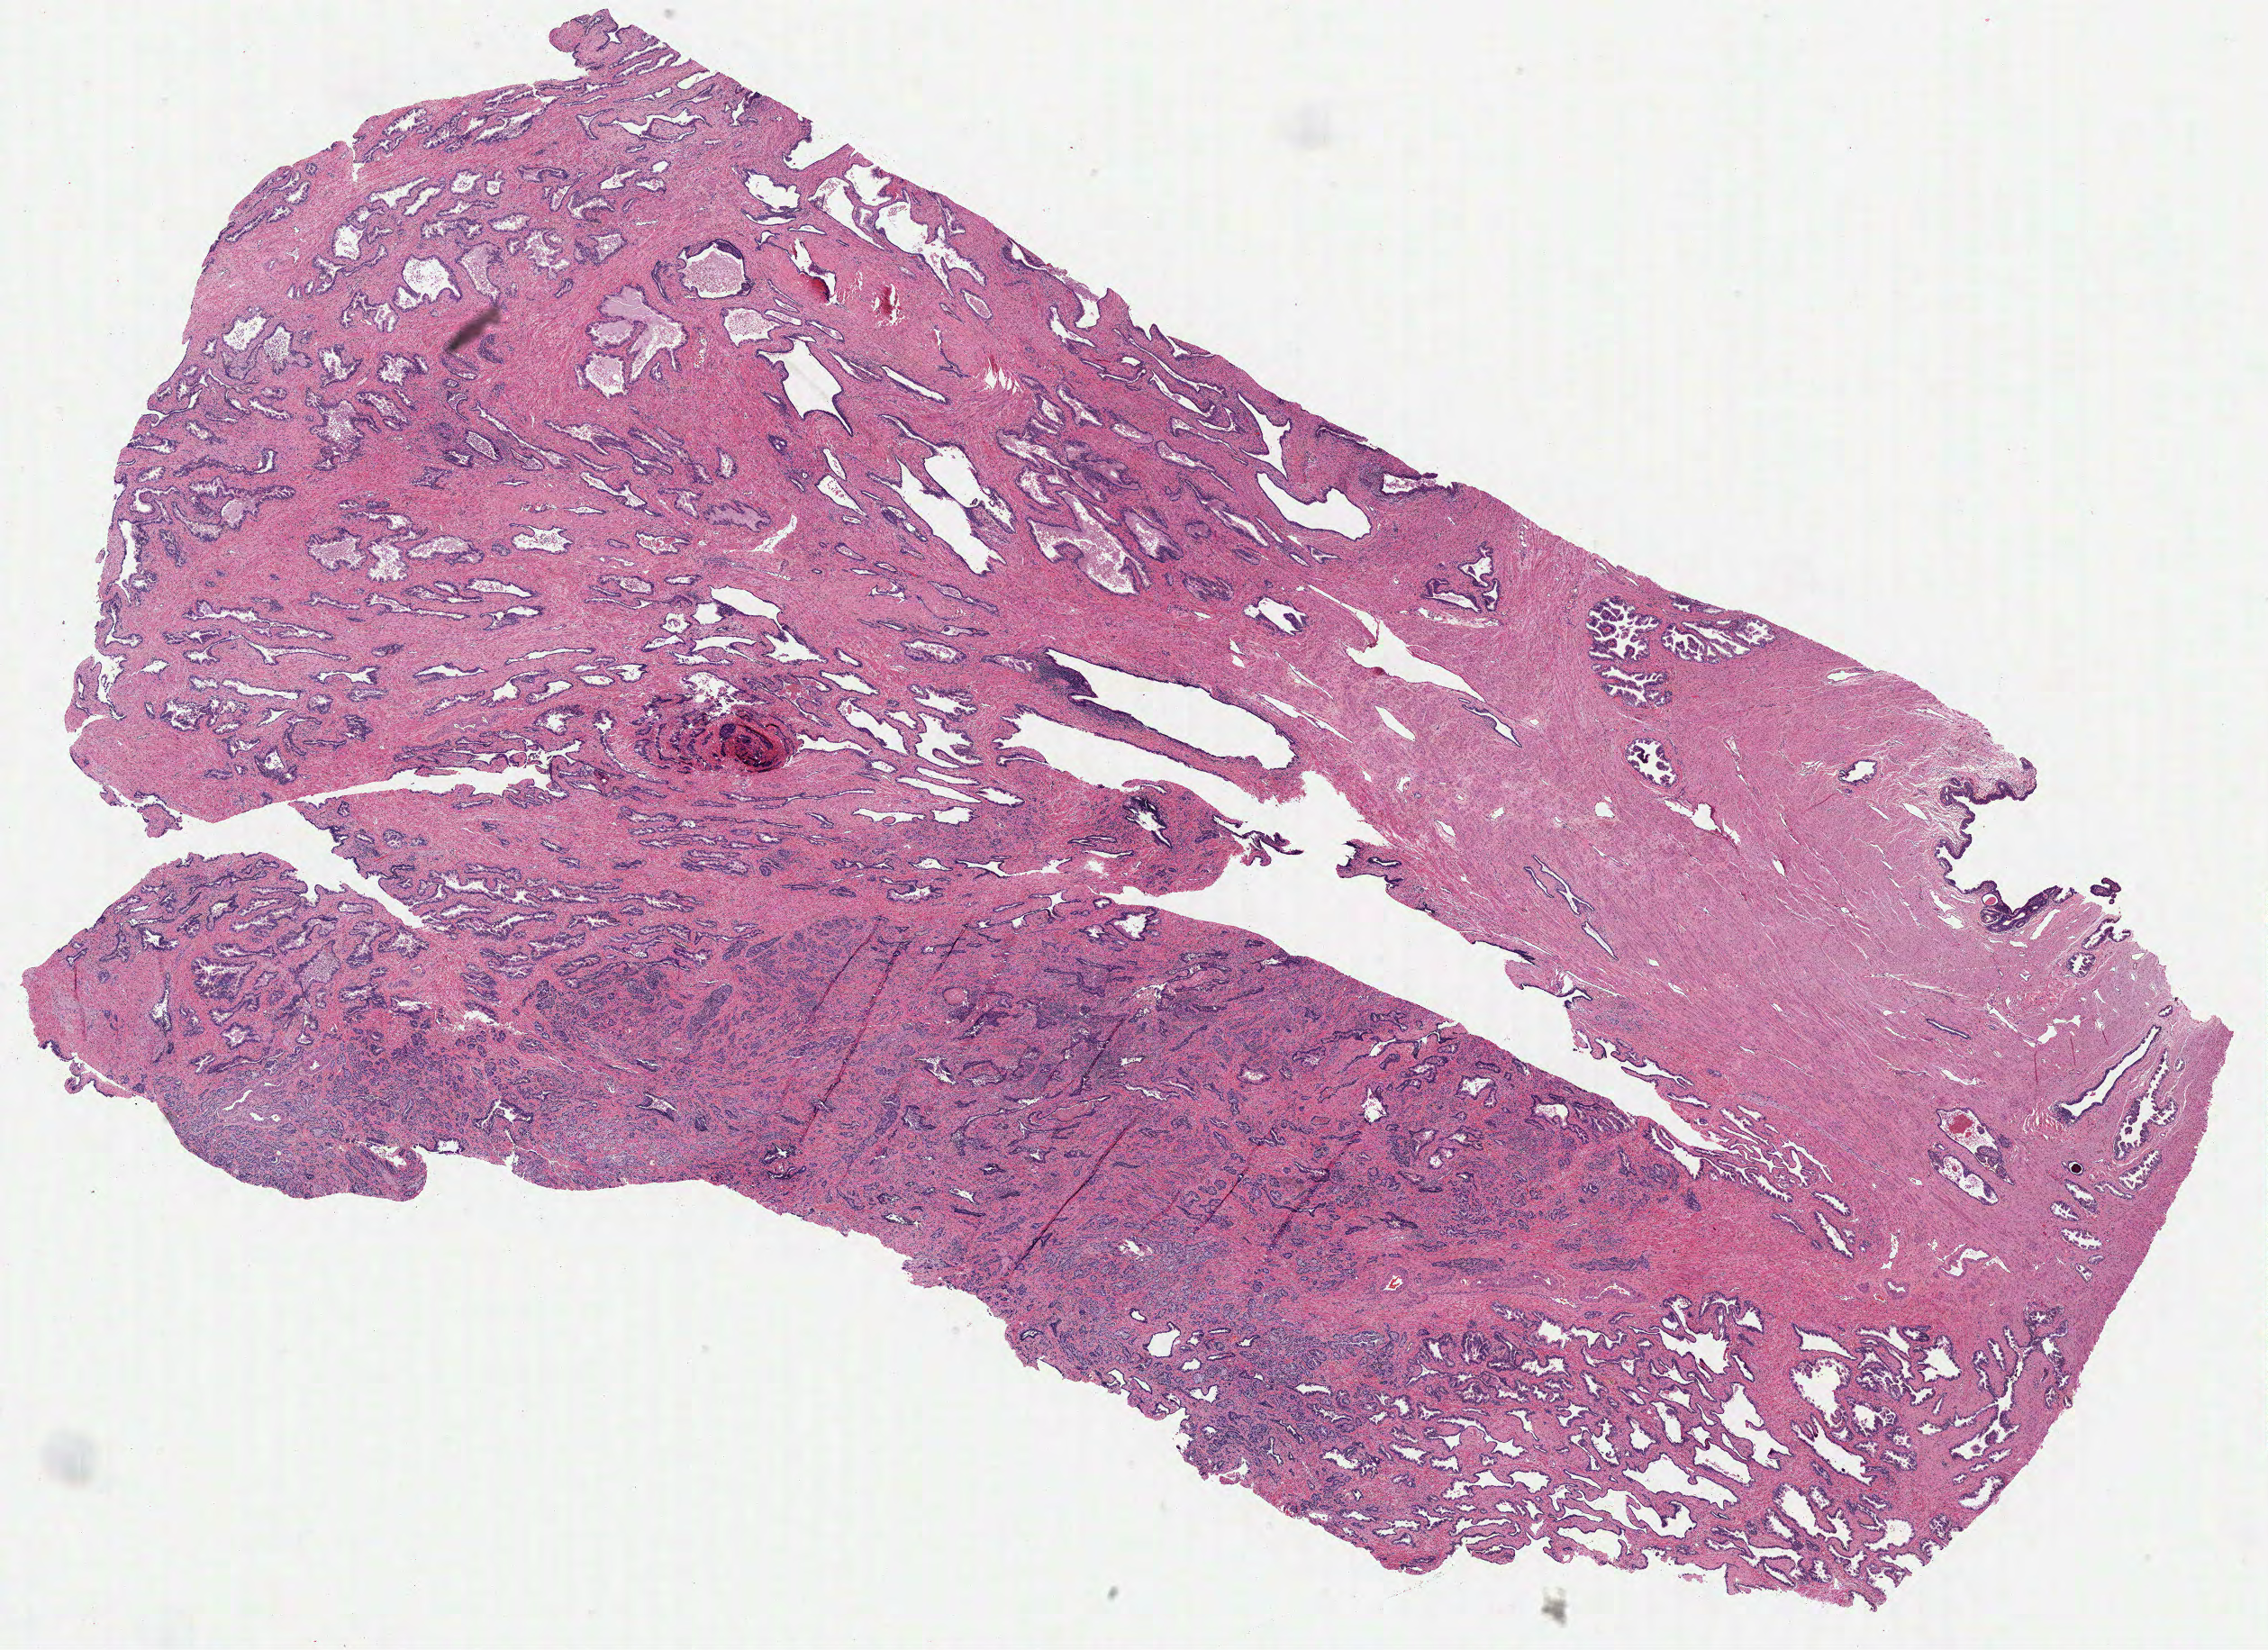
Whole-slide histology image, H&E-stained — whole scanned area (about 20.3 x 14.8 mm, slide scanned at 40x) shown as a low-resolution overview. FFPE section. Primary tumour sample from the prostate. Male, age 70 years at initial diagnosis. Gleason score: 7 (4+3).
• laterality: bilateral
• diagnosis: Acinar cell carcinoma (prostate gland)
• lymph nodes positive (case pathology): 0 of 9 examined